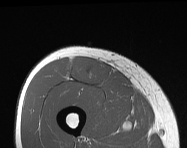
MRI of an extremity soft-tissue mass, one axial slice. Slice 57 of 114 in the series (ordered by position). MR volume resampled by the dataset authors to the PET/CT grid (not the native acquisition matrix). 3.27 mm slice thickness. 187 × 148 image matrix, field of view 183 × 145 mm. Male patient. From the clinical record (not read from this slice): histological type: pleiomorphic leiomyosarcoma; grade: intermediate; site of the primary tumour: right thigh.
Outlined on this slice (expert contour drawn on MRI and transferred to this co-registered scan by the dataset authors):
- gross tumour volume including surrounding oedema: bounding box <70,56,110,85> (left, top, right, bottom; pixels)